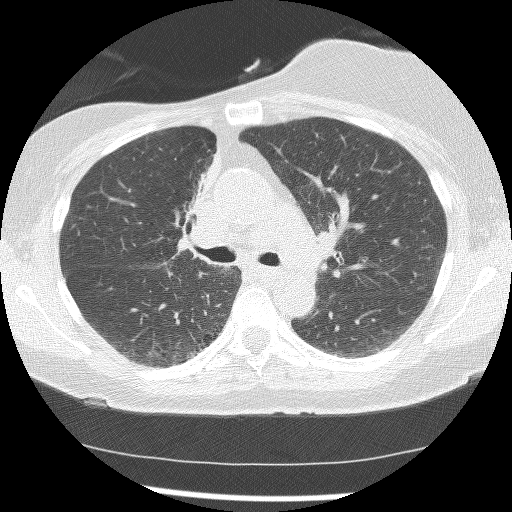
Axial slice from a low-dose chest CT screening exam. Baseline annual screen. Lung window (W 1500 / L -600 HU). Lung (sharp) reconstruction kernel (BONE). 120 kVp. Female participant, aged 56 years at enrolment.
Expert reader's lesion annotation, bounding box (x1, y1, x2, y2) in pixels: (162, 154, 218, 260). The screening reader recorded 2 non-calcified nodules or masses ≥4 mm on this exam (right lower lobe, right middle lobe); which of them this box marks is not recorded. Official screen result: positive, change unspecified: nodule(s) >= 4 mm or enlarging nodule(s), mass(es), or other non-specific abnormalities suspicious for lung cancer.